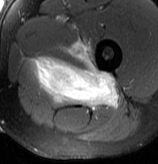
MRI of an extremity soft-tissue mass, one axial slice. Position 54 of 70 along the scan axis. T2-weighted fat-saturated. MR volume resampled by the dataset authors to the PET/CT grid (not the native acquisition matrix). 3.27 mm slice thickness. 158 × 164 image matrix, field of view 154 × 160 mm. Male patient. Case-level facts recorded for this patient, not image findings: histological type: extraskeletal osteosarcoma; grade: high; site of the primary tumour: left adductur.
Outlined on this slice (expert contour drawn on MRI and transferred to this co-registered scan by the dataset authors):
- gross tumour volume (mass): bounding box (x1, y1, x2, y2) in pixels: (31, 39, 119, 109)